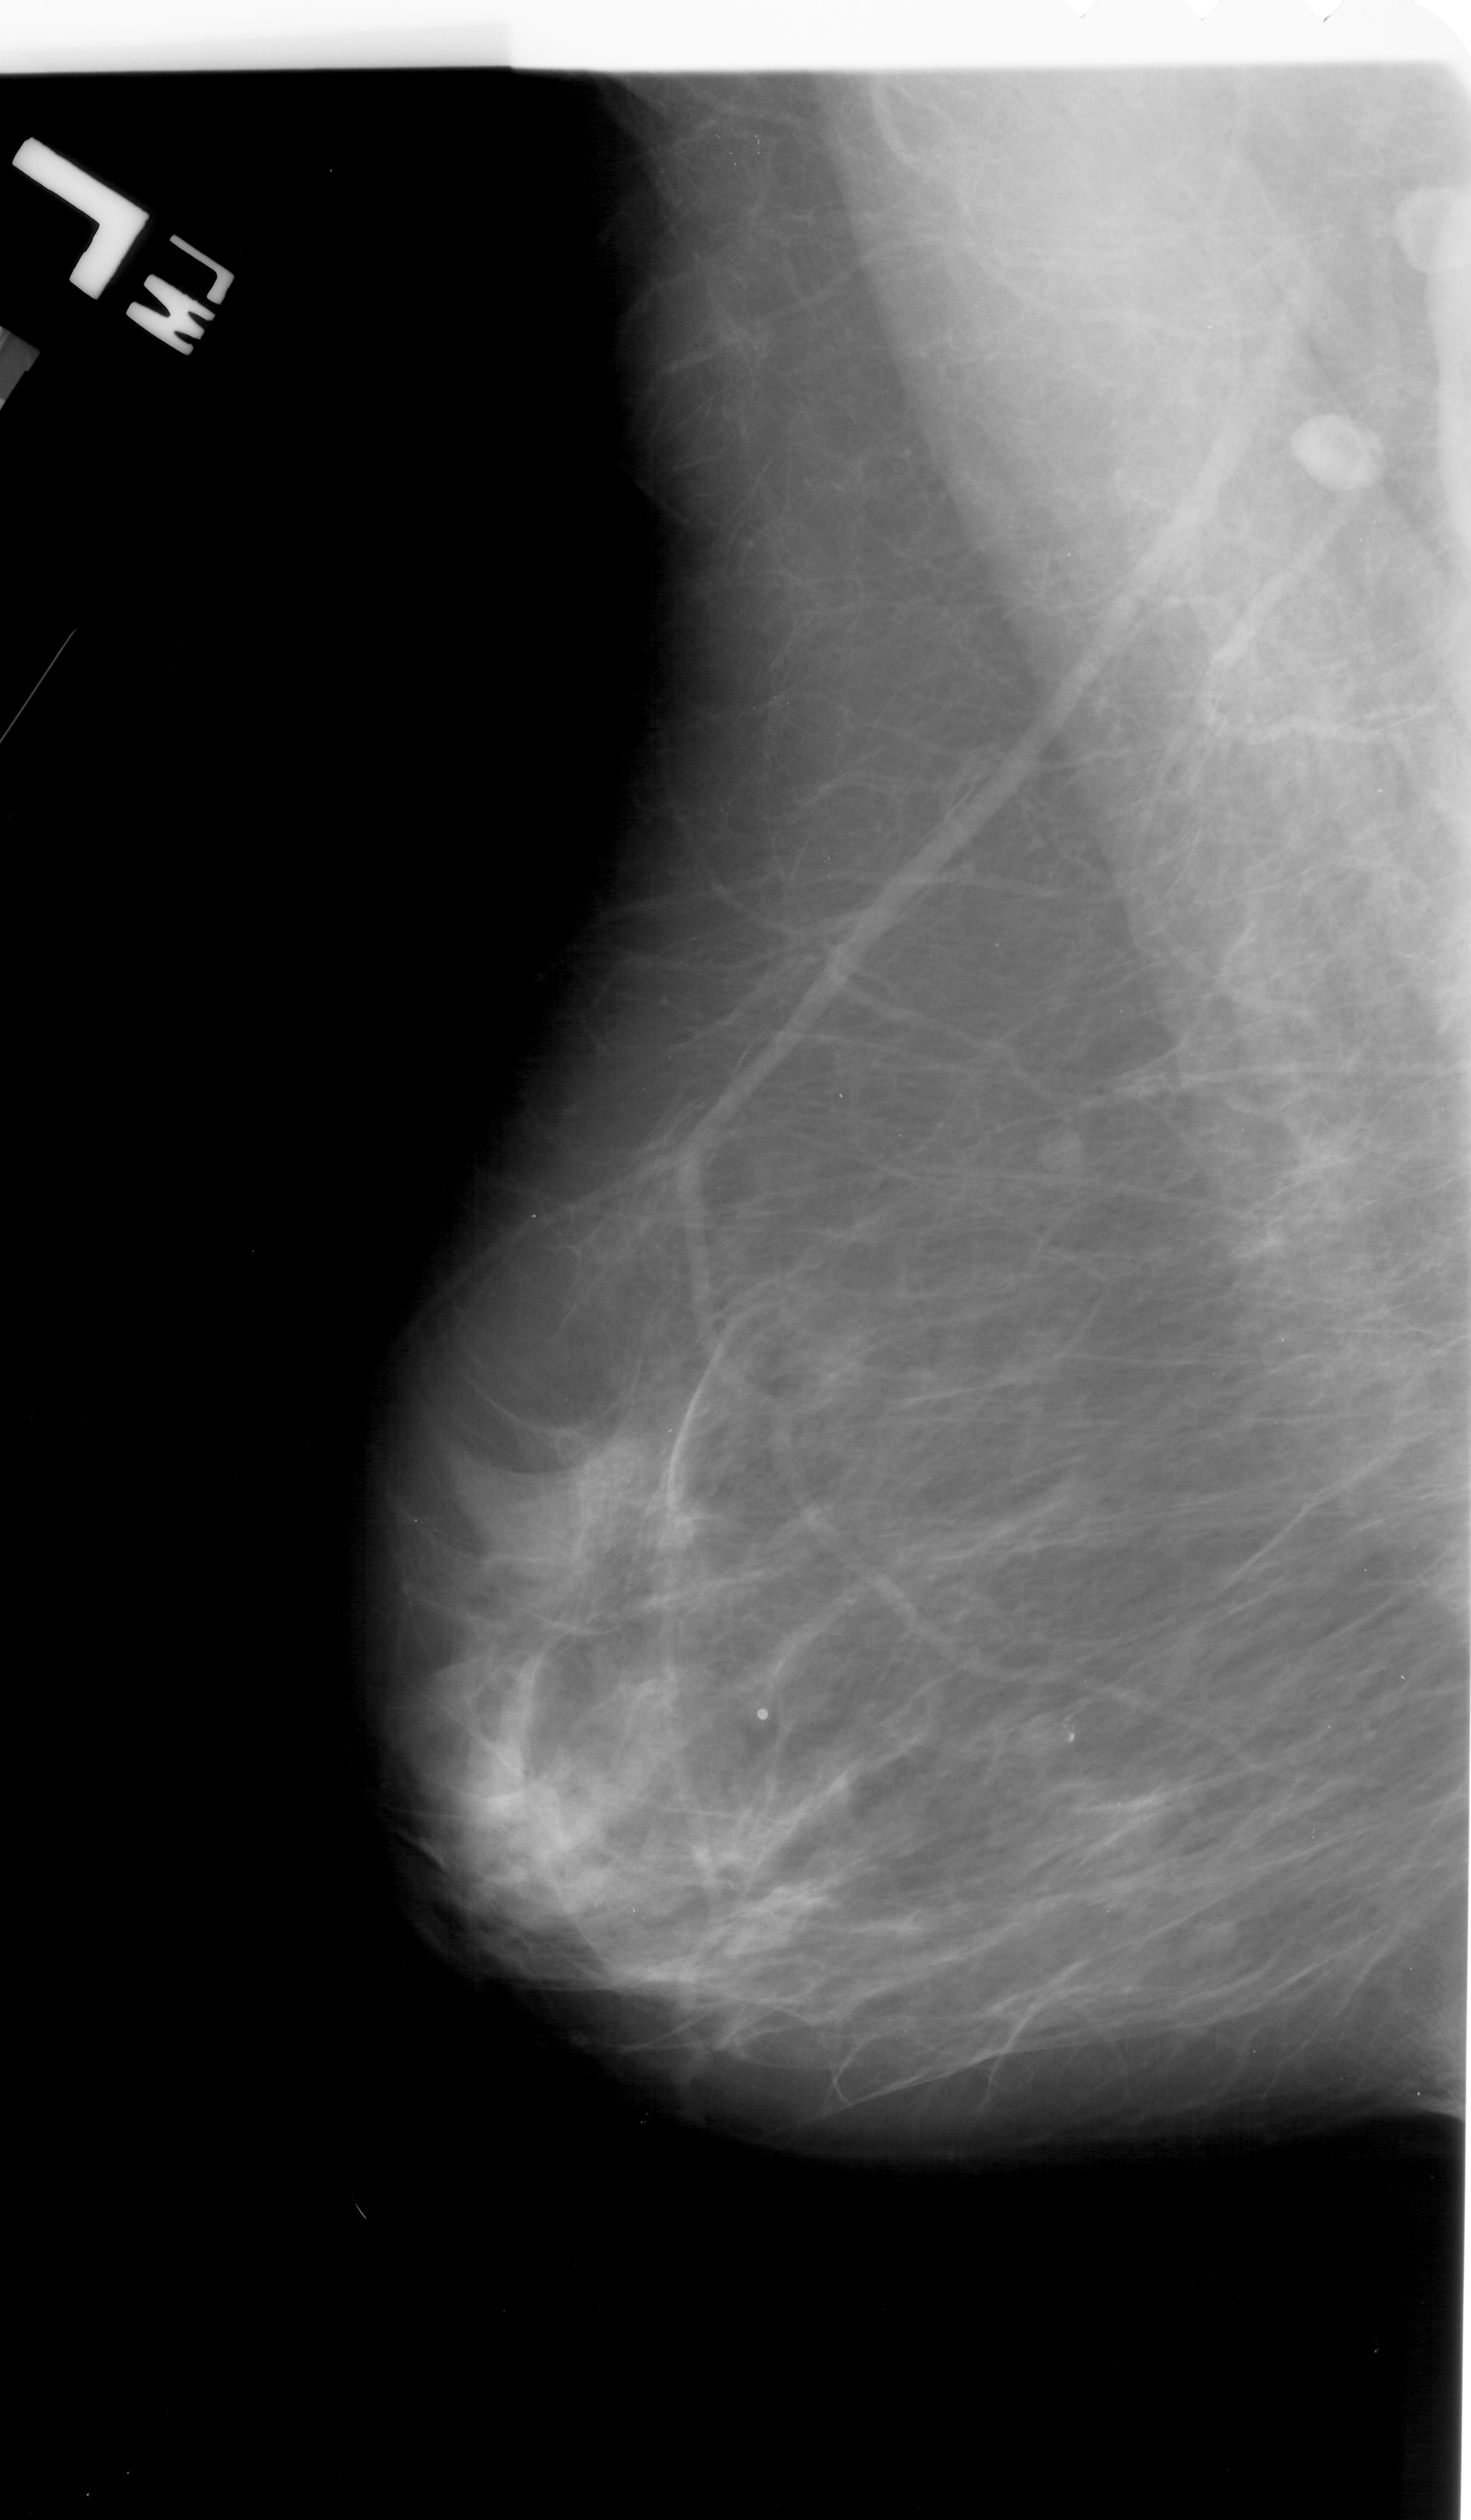
Mammogram (digitized film); left breast; mediolateral oblique (MLO) view; breast composition: scattered fibroglandular densities (BI-RADS density category 2 of 4).
Finding: calcifications, morphology pleomorphic, distribution linear; BI-RADS assessment category 4; subtlety rating 1 on a 1 (subtle) to 5 (obvious) scale; pathology result (as recorded, not read from the image): malignant.